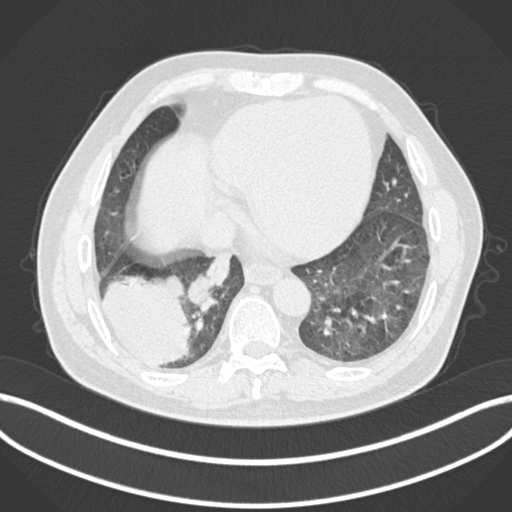
Chest CT, one axial slice; position 42 of 200 along the scan axis; reconstruction kernel B30f; 120 kVp; lung window (W 1500 / L -600 HU); 512 × 512 image matrix. Male patient, age 59 years.
Structures marked on this image (rectangle marked by the reading radiologist):
- lung tumour (recorded histology: adenocarcinoma): bounding box <94,270,195,366> (left, top, right, bottom; pixels)